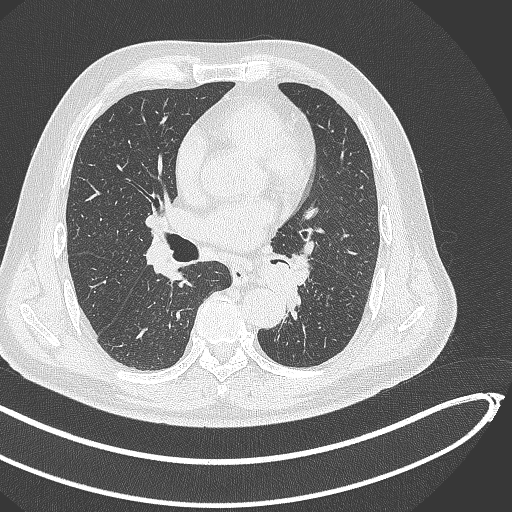
Chest CT, one axial slice. Slice 247 of 468 in the series (ordered by position). 120 kVp. Lung window (W 1500 / L -600 HU). 512 × 512 image matrix, field of view 400 × 400 mm. Patient: male, 64 years. From the clinical record (not read from this slice): clinical TNM (as recorded): T1c N0 M0; histopathological grade: G2.
Annotated regions visible in this slice (bounding box drawn by a radiologist):
- lung tumour (recorded histology: squamous cell carcinoma): bounding box (x1, y1, x2, y2) in pixels: (255, 258, 308, 325)